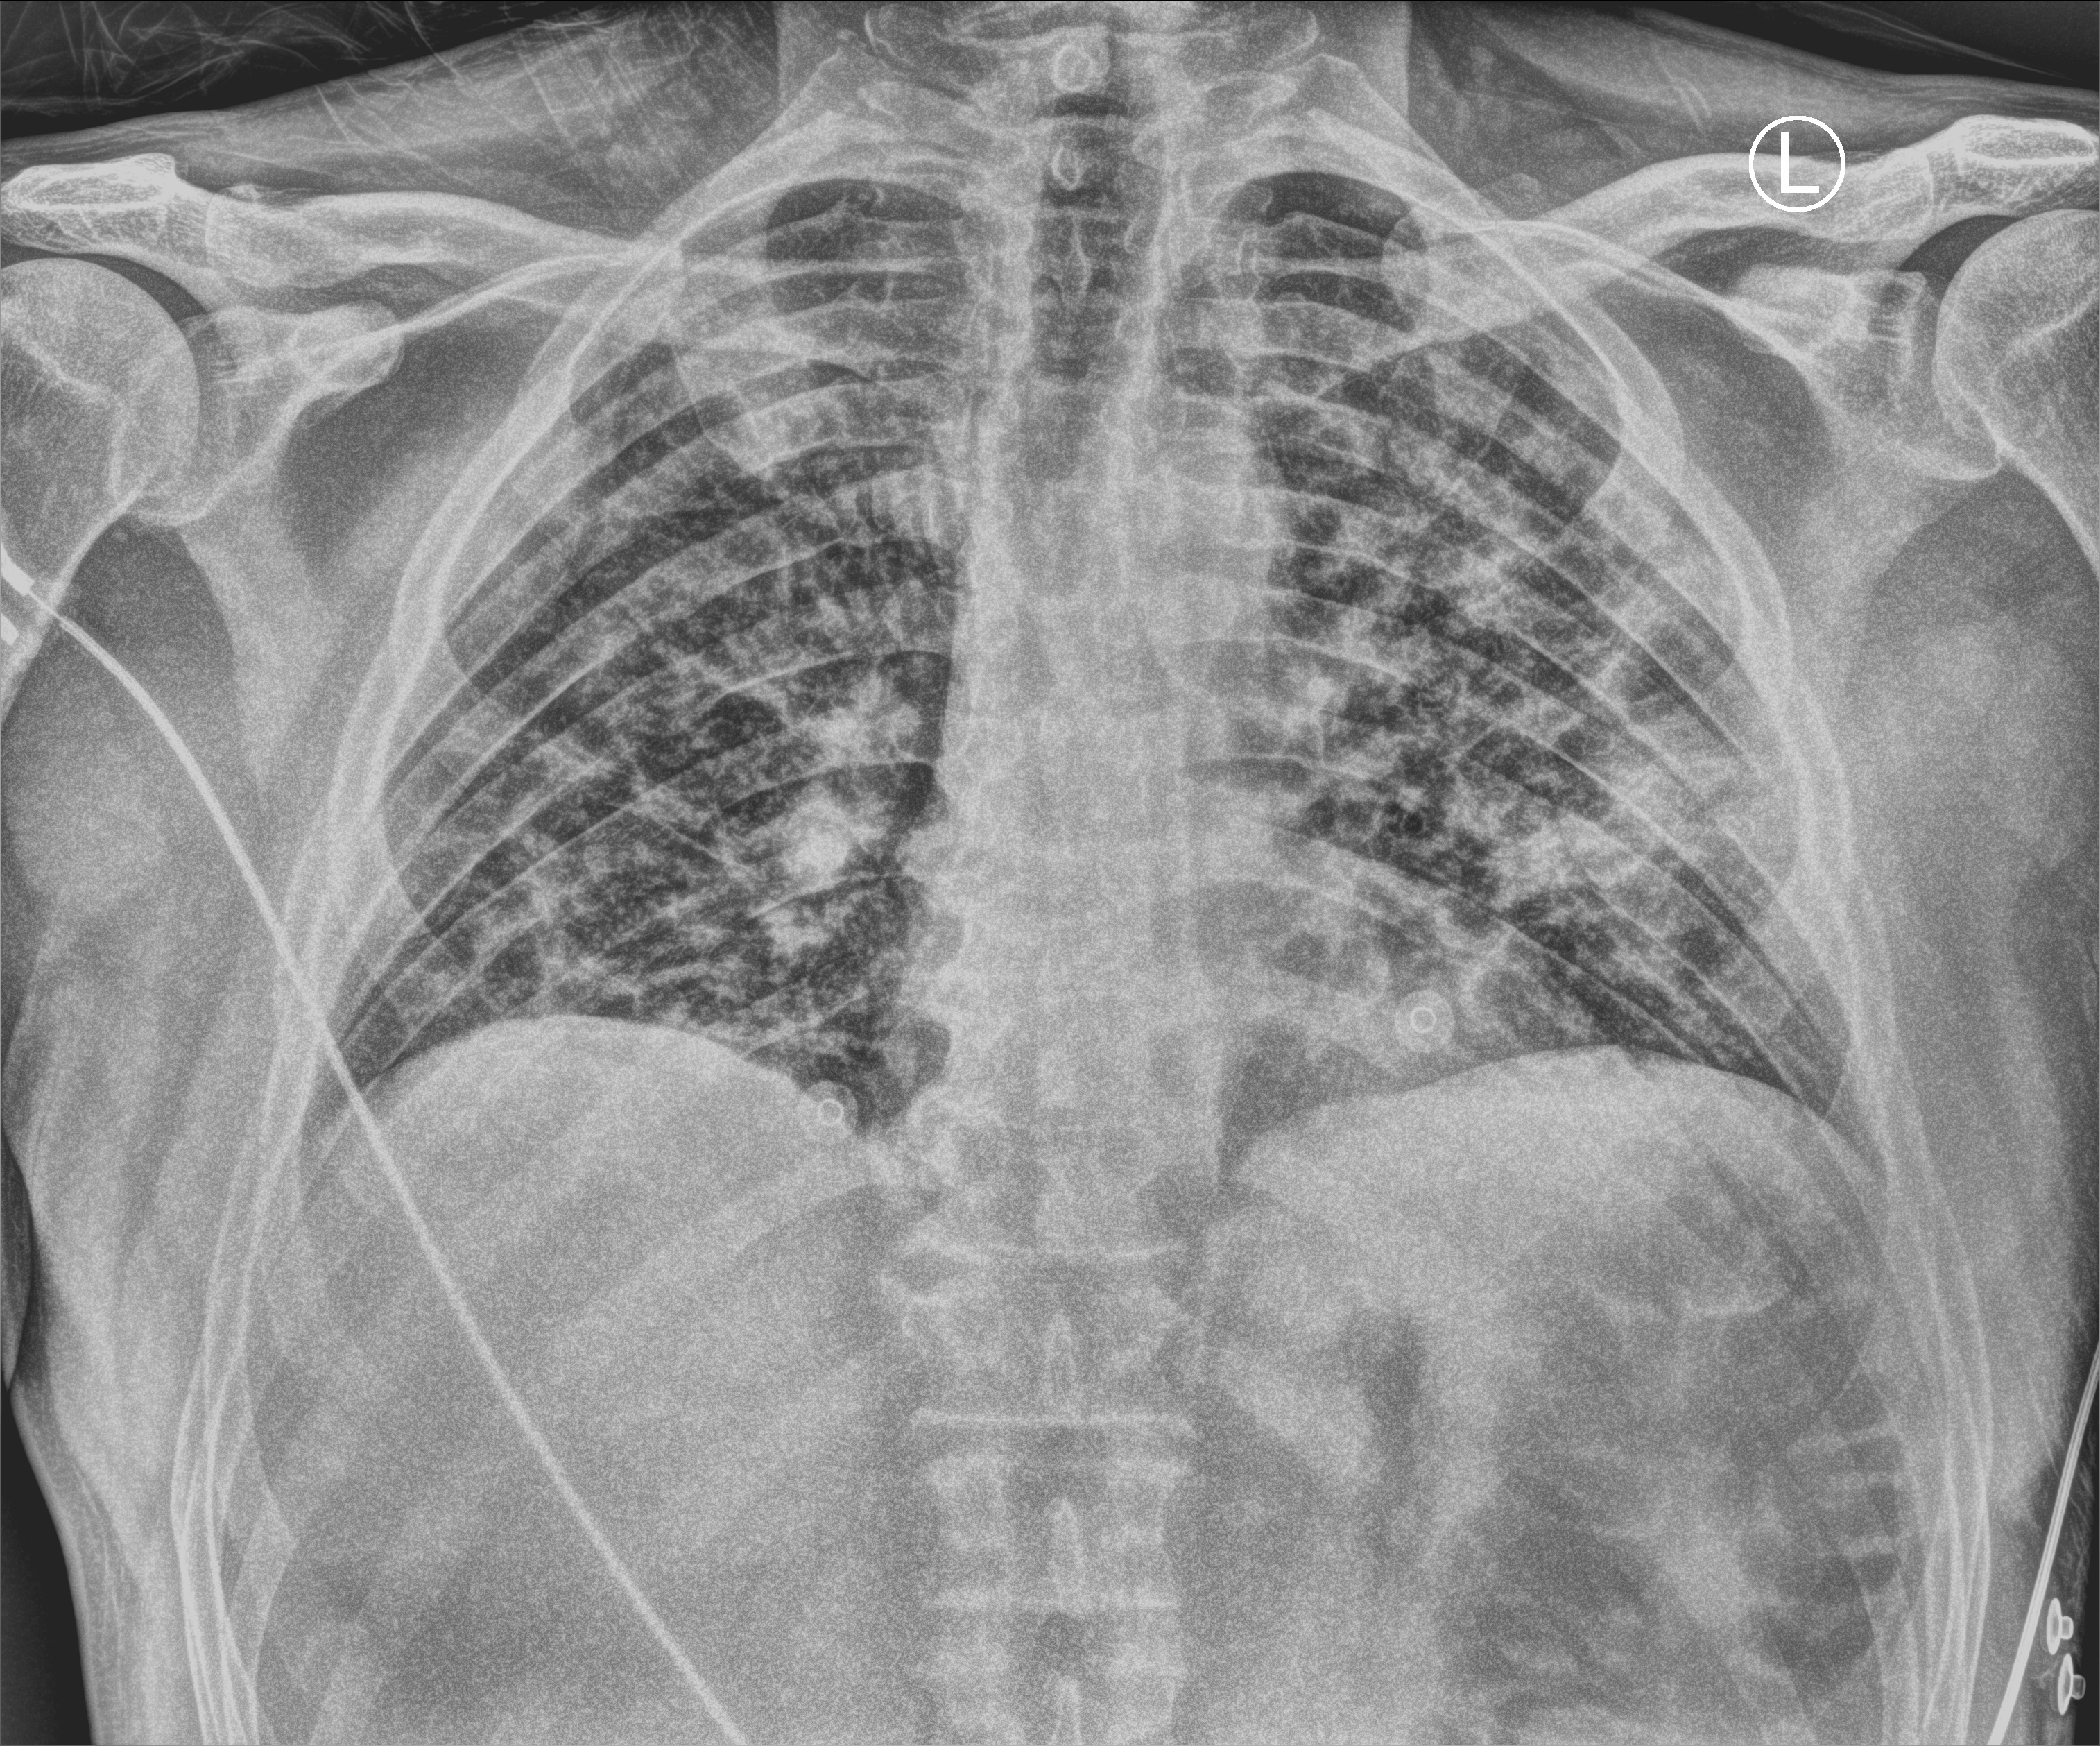
Bedside chest radiograph (computed radiography). Patient hospitalised with COVID-19; male, aged 18–59 years.
From the hospital-stay record, not from the radiograph (when in the stay this image was taken is not recorded): chronic kidney disease (admission record): no; length of hospital stay: 9 days; admitted to intensive care during this hospital stay: no.